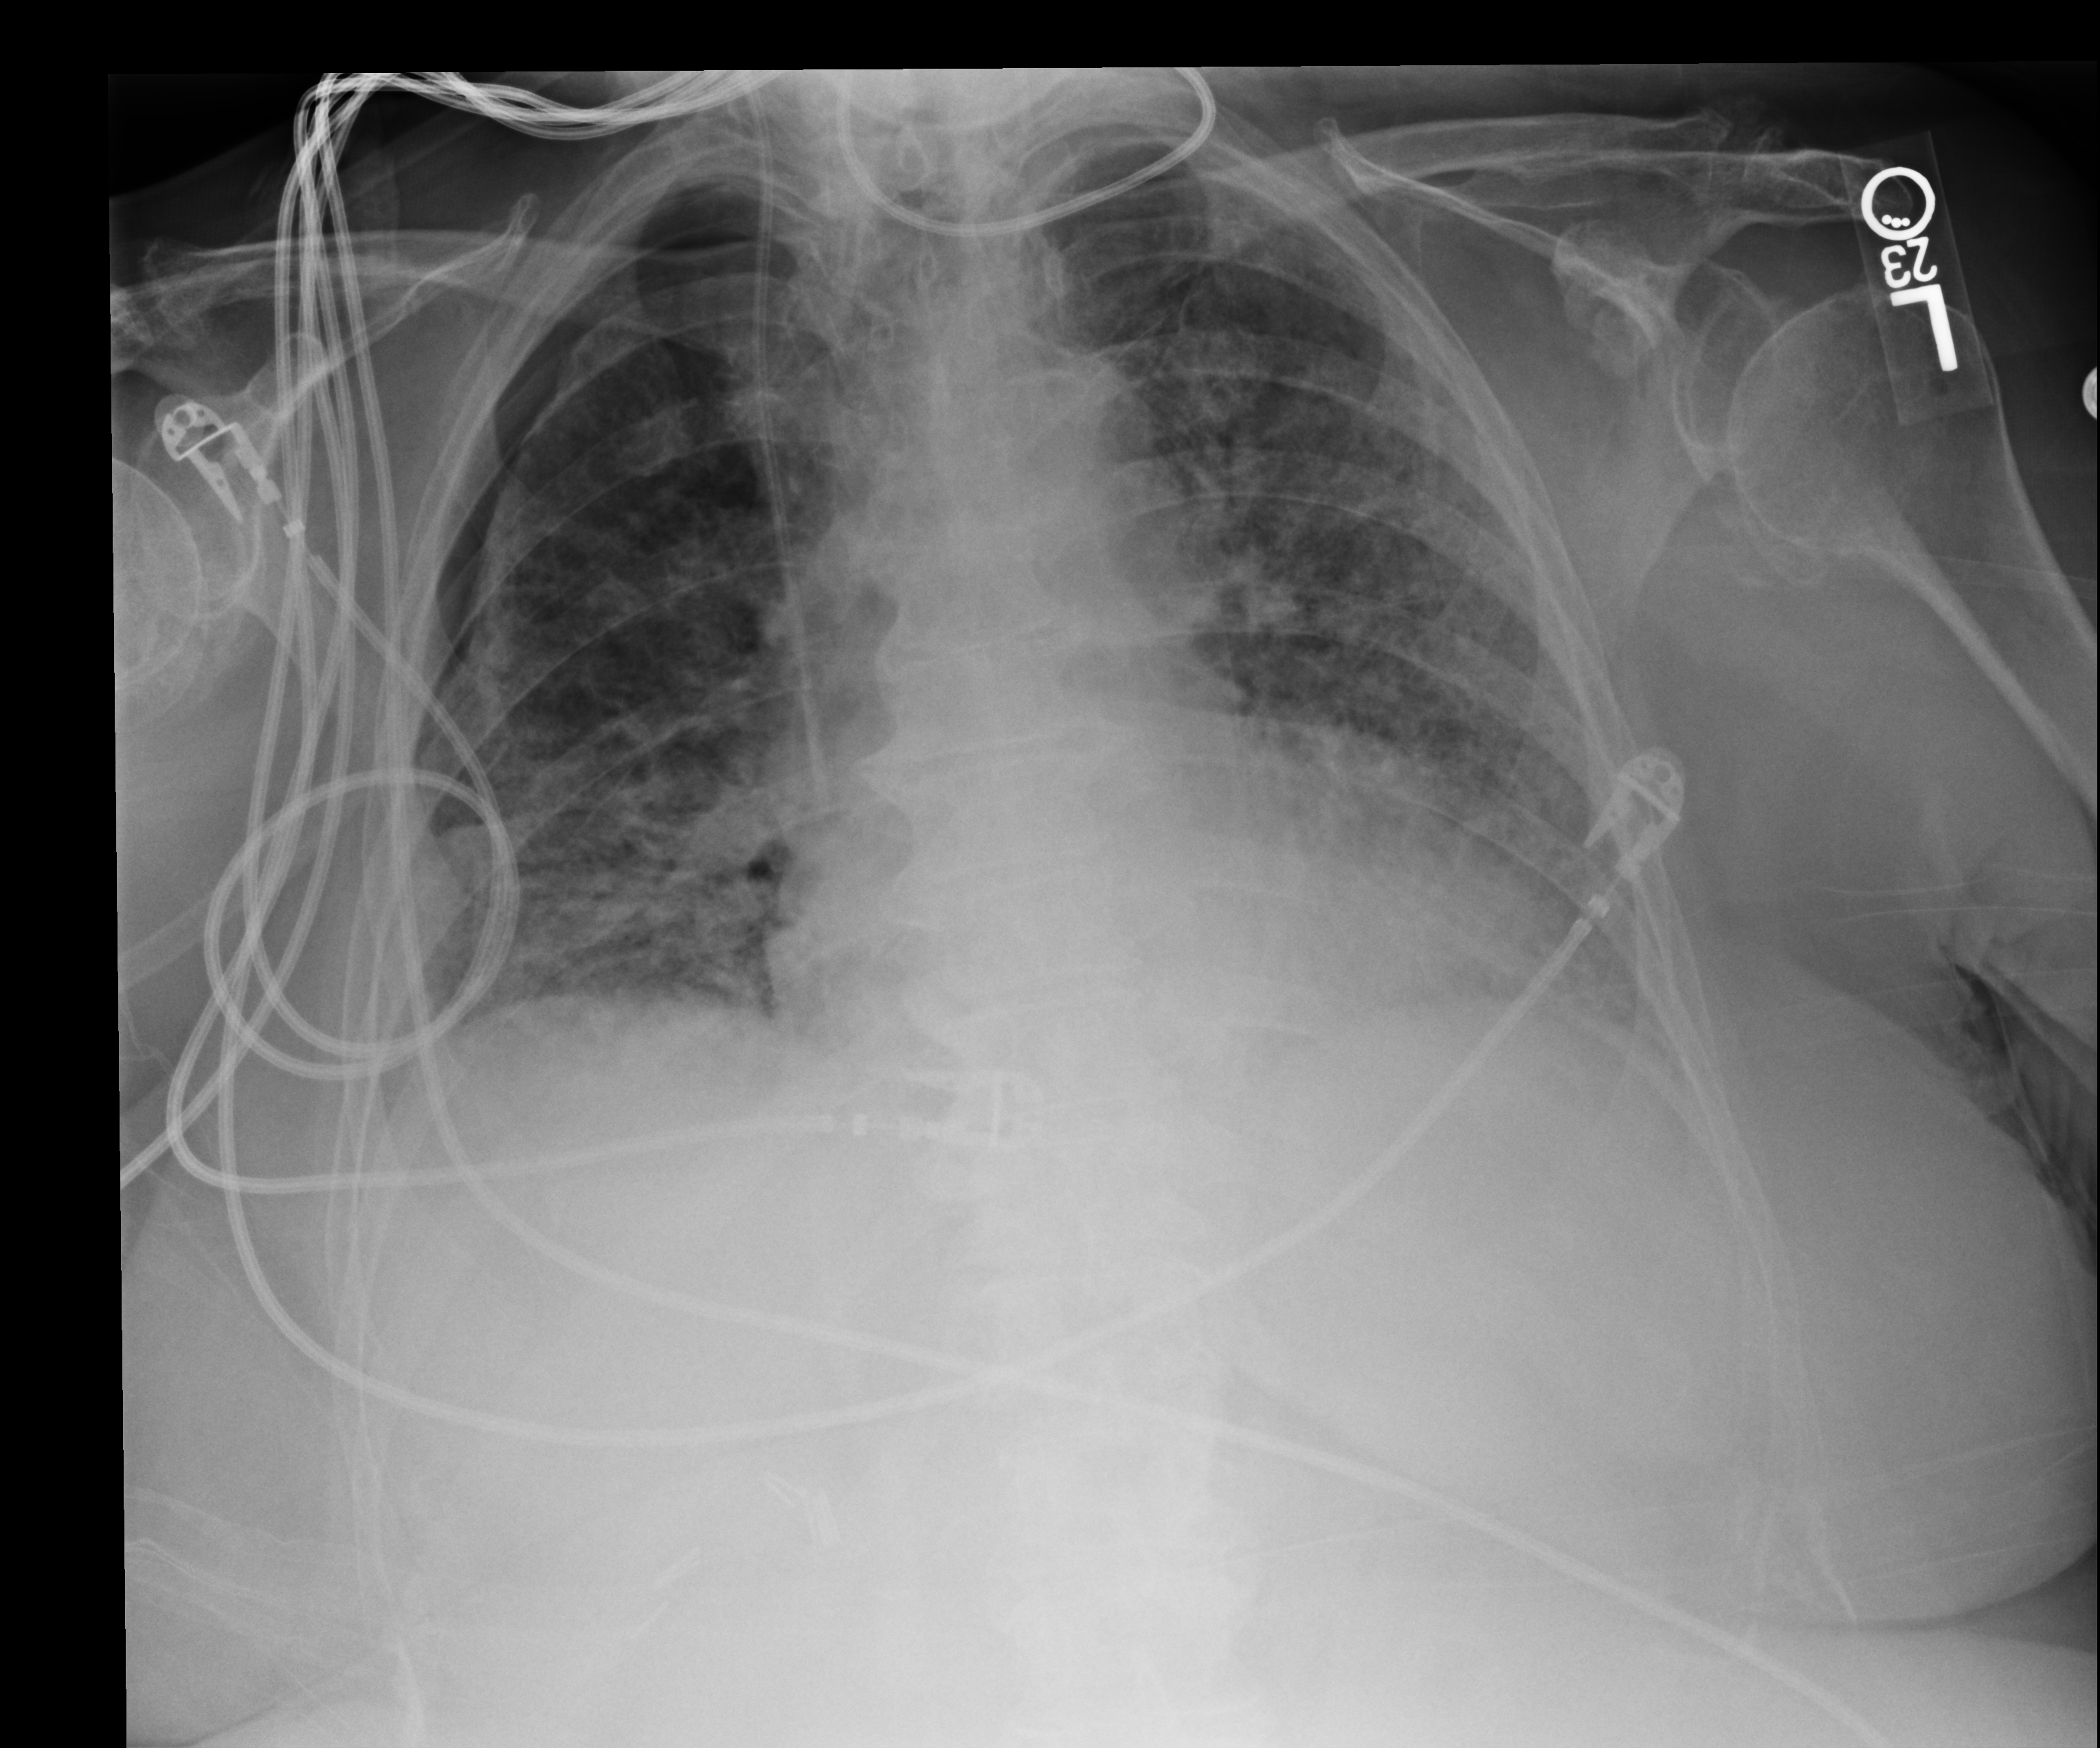
Chest X-ray (portable), anteroposterior (AP) projection. Patient hospitalised with COVID-19; female, aged 75–90 years.
From the hospital-stay record, not from the radiograph (when in the stay this image was taken is not recorded): length of hospital stay: 56 days; admitted to intensive care during this hospital stay: no; mechanically ventilated during this hospital stay: yes.